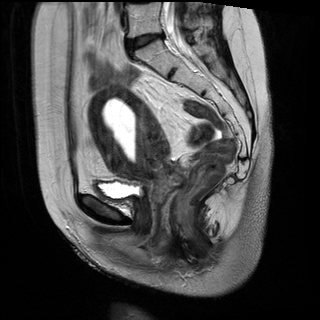
Pelvic MRI for cervical cancer, one sagittal slice; slice 14 of 28 in the series (ordered by position); T2-weighted; 1.5 T; TE 89 ms, TR 2740 ms; 4 mm slice thickness; 320 × 320 image matrix, field of view 260 × 260 mm. Female patient, age 49 years.
Structures marked on this image (expert manual segmentation):
- uterus and cervix: bounding box <87,85,188,206> (left, top, right, bottom; pixels)